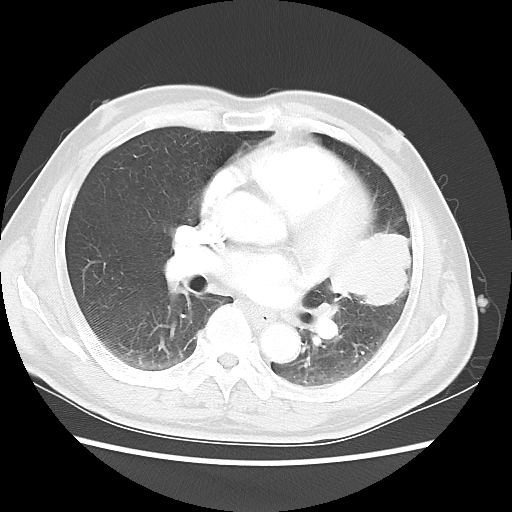
Chest CT, one axial slice; slice 25 of 50 in the series (ordered by position); lung window (W 1500 / L -600 HU); 512 × 512 image matrix. Patient: male, 69 years. Case-level facts recorded for this patient, not image findings: clinical TNM (as recorded): T3 N1 M1a.
Annotated regions visible in this slice (bounding box drawn by a radiologist):
- lung tumour (recorded histology: squamous cell carcinoma): box from (x=319, y=218) to (x=419, y=327) px